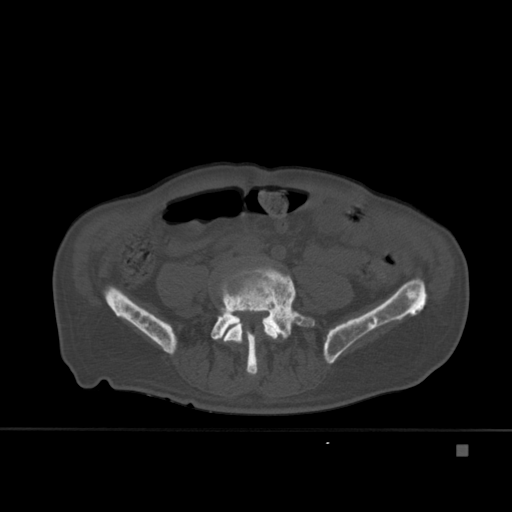
CT including the spine, one axial slice. Position 110 of 451 along the scan axis. Bone window (W 1800 / L 400 HU). 512 × 512 image matrix, field of view 378 × 378 mm. Patient: male, 75 years. Case-level facts recorded for this patient, not image findings: primary cancer: prostate.
Annotated regions visible in this slice (semi-automatic segmentation, software-assisted and operator-edited):
- L4 vertebra: bounding box [x1, y1, x2, y2] px = [223, 311, 279, 376]
- L5 vertebra: [211, 265, 315, 374]
- T7 vertebra: [266, 312, 275, 325]